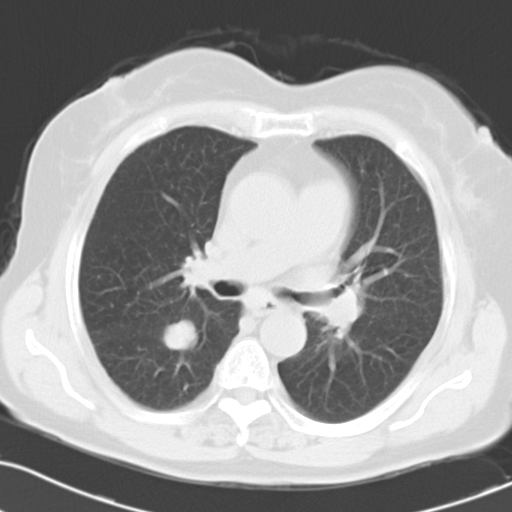
Chest CT, one axial slice. Position 17 of 27 along the scan axis. Reconstruction kernel B40f. 120 kVp. Lung window (W 1500 / L -600 HU). 10 mm slice thickness. 512 × 512 image matrix, field of view 323 × 323 mm. Patient: female, 70 years. Case-level facts recorded for this patient, not image findings: clinical TNM (as recorded): T1c N3 M0.
Outlined on this slice (rectangle marked by the reading radiologist):
- lung tumour (recorded histology: small cell carcinoma): box from (x=154, y=306) to (x=201, y=358) px